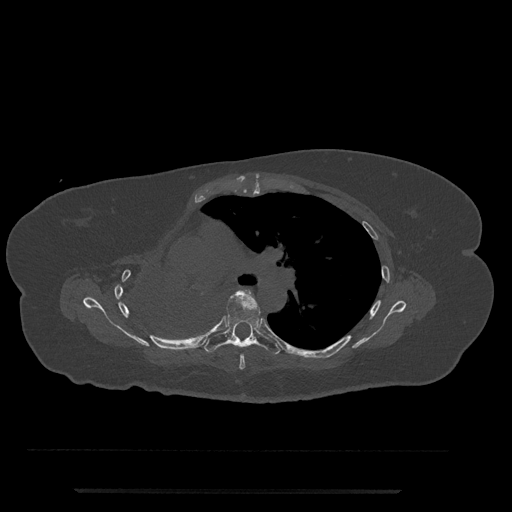
CT including the spine, one axial slice; position 508 of 797 along the scan axis; 120 kVp; bone window (W 1800 / L 400 HU); 512 × 512 image matrix. Patient: female, 51 years. From the clinical record (not read from this slice): primary cancer: neuro.
Annotated regions visible in this slice (semi-automatic segmentation, software-assisted and operator-edited):
- T5 vertebra: bounding box <239,319,265,370> (left, top, right, bottom; pixels)
- T6 vertebra: <205,293,281,355>